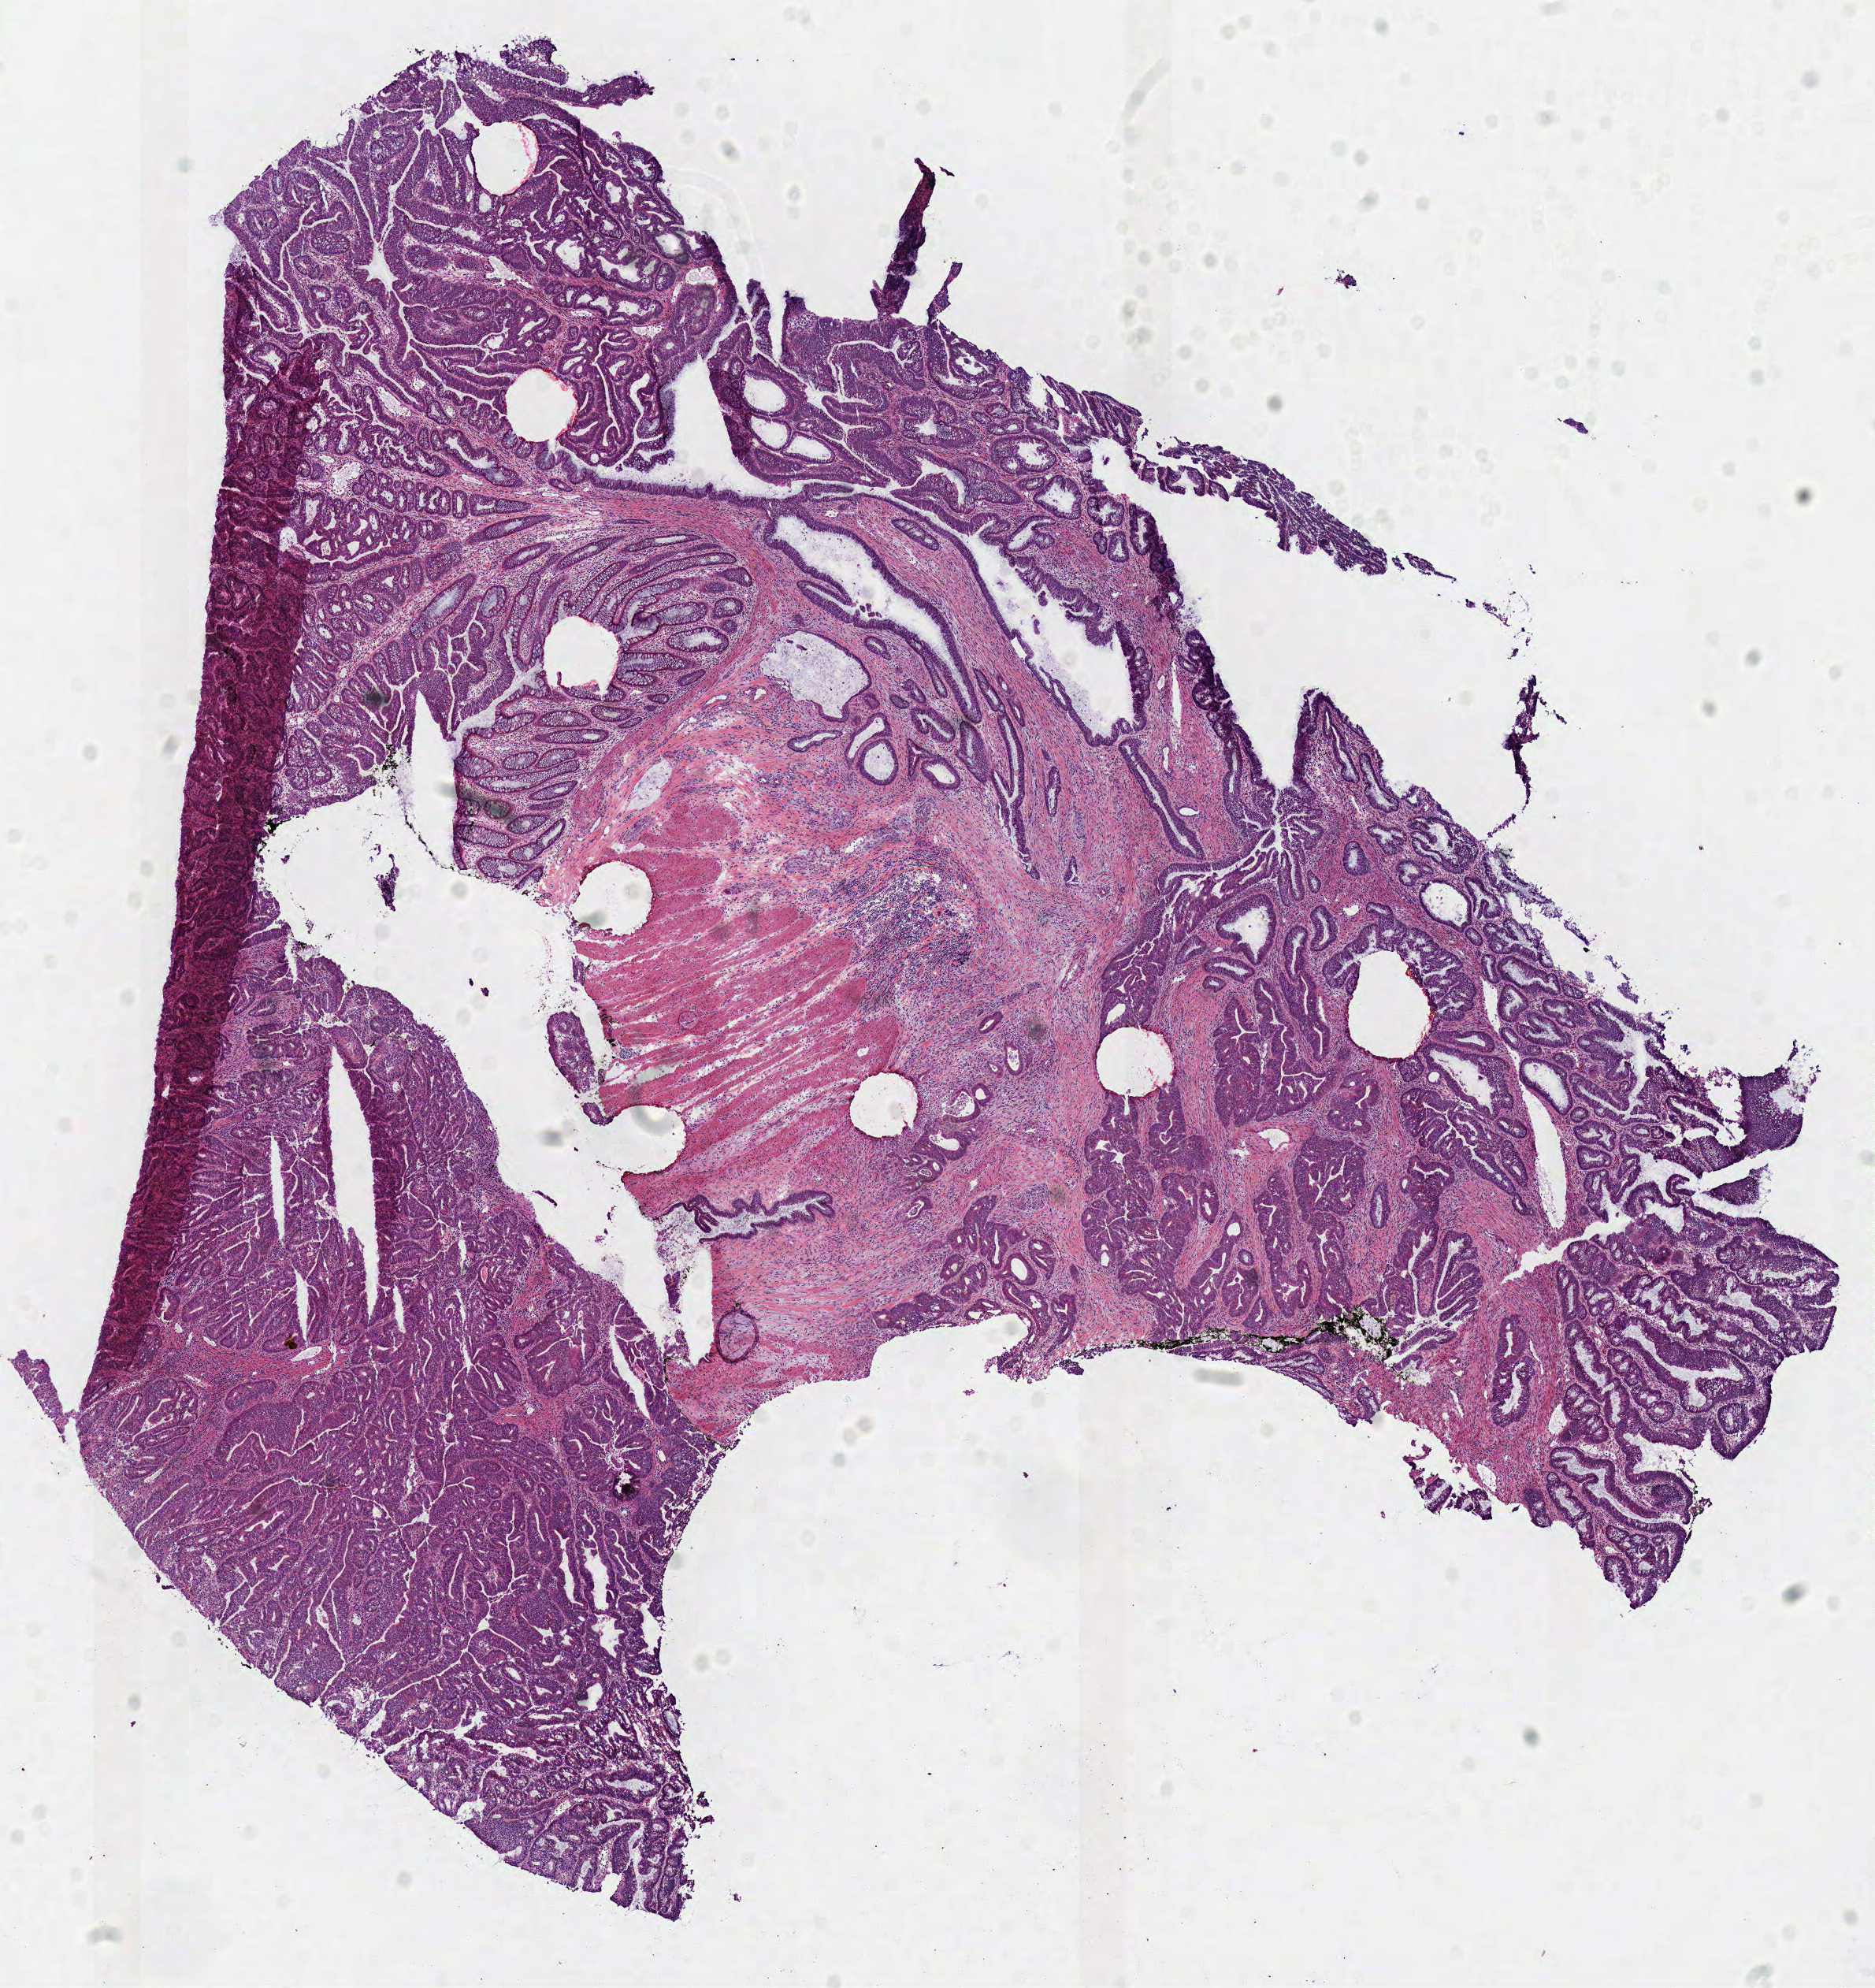
H&E-stained whole-slide image, a low-resolution overview of the entire scanned area, about 9.4 x 9.9 mm (acquisition: 40x scan), frozen section from the top of the tissue portion, rectum, primary tumour sample. Male patient; age at initial diagnosis 46 years. Composition of this section per pathologist review: tumour cells 69%, tumour nuclei 75%, normal cells 3%, stromal cells 25%, necrosis 3%.
TNM: T3 N1b M0. AJCC pathologic stage: IIIB (7th edition). Histologic diagnosis: Mucinous adenocarcinoma (rectosigmoid junction).